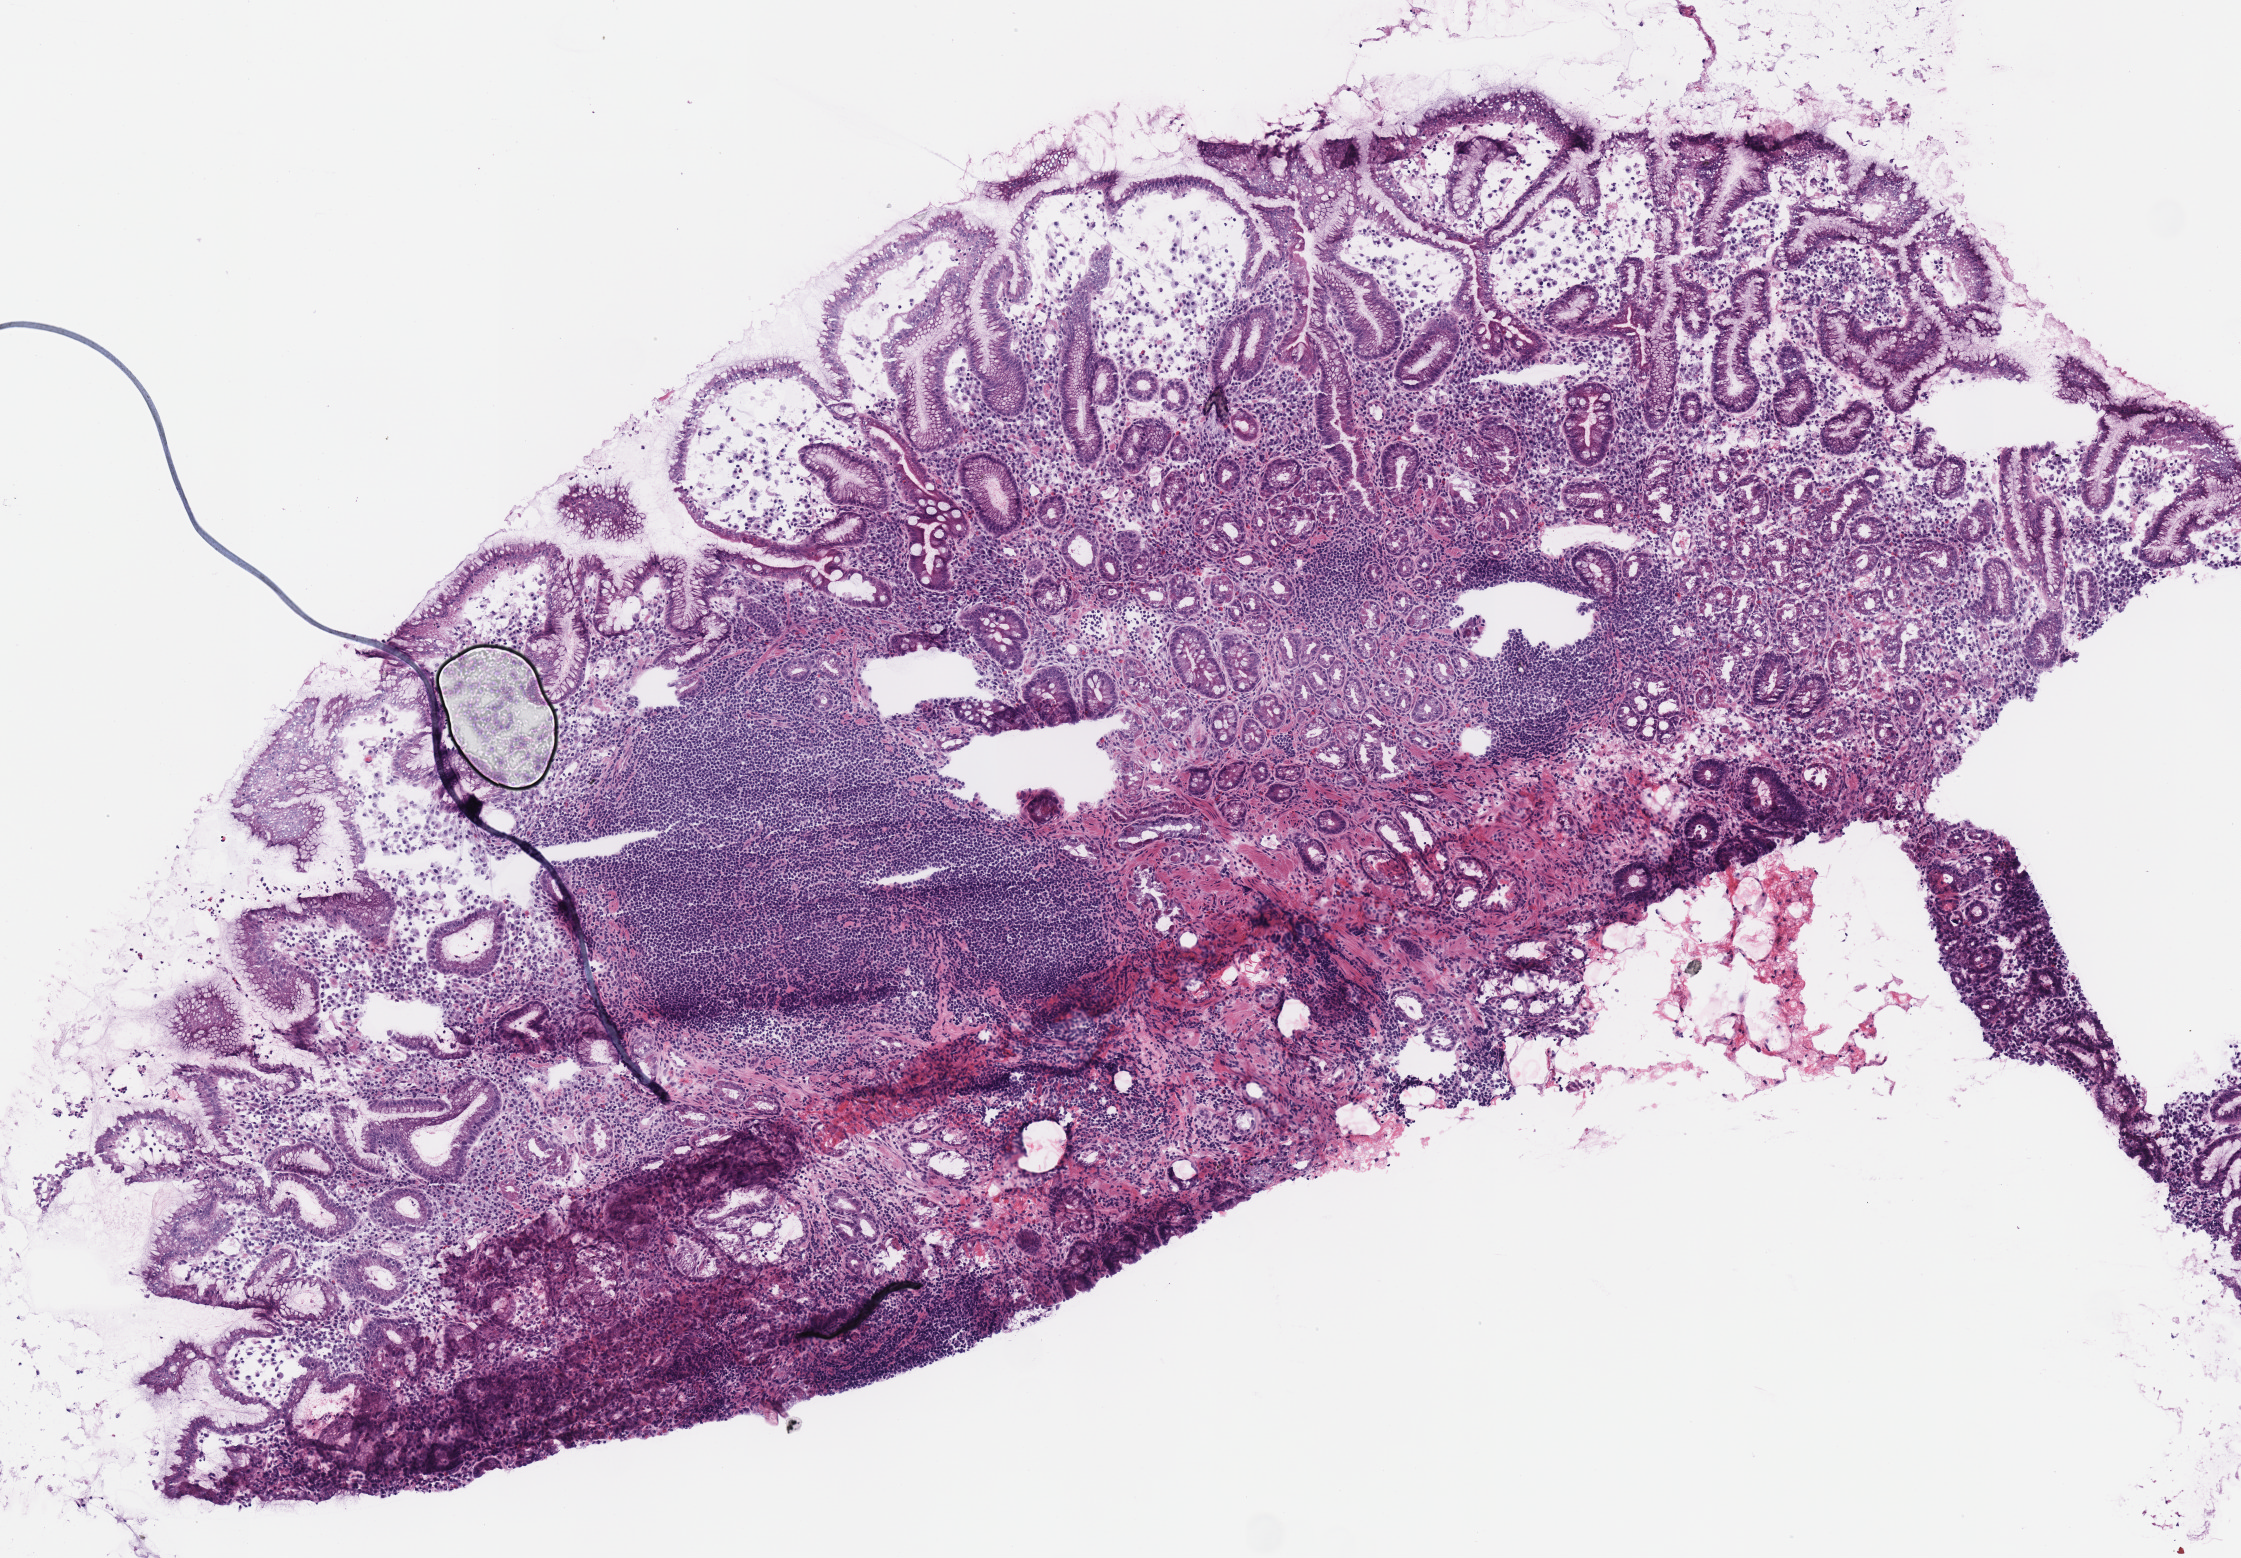
Hematoxylin and eosin (H&E) stained whole-slide image — shown as a low-resolution overview of the whole scanned area (about 4.4 x 3.1 mm); frozen section; solid tissue normal (non-tumour tissue) sample from the stomach. Male, age 70 years at initial diagnosis.
• this section: solid tissue normal (non-tumour) sample from the same patient
• patient diagnosis: Carcinoma, diffuse type (body of stomach)